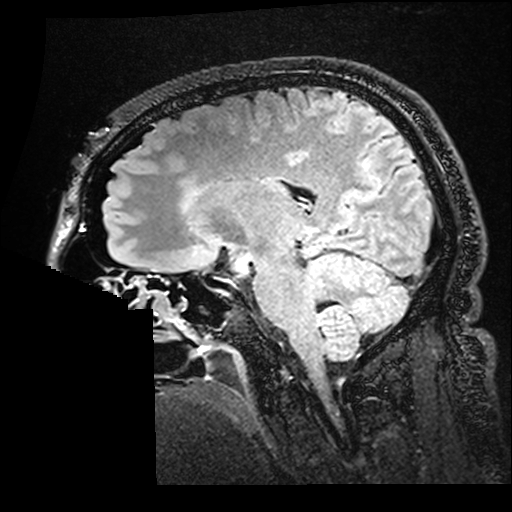
Brain MRI from a brain-tumour surgery series, one sagittal slice. Position 104 of 176 along the scan axis. T2 FLAIR. 1 mm slice thickness. 512 × 512 image matrix, field of view 250 × 250 mm. From the clinical record (not read from this slice): histopathology: Astrocytoma; WHO grade: 2; IDH mutation: yes; tumour location: Right Insular.
Annotated regions visible in this slice (expert manual segmentation):
- residual tumour: bounding box <192,191,197,195> (left, top, right, bottom; pixels)